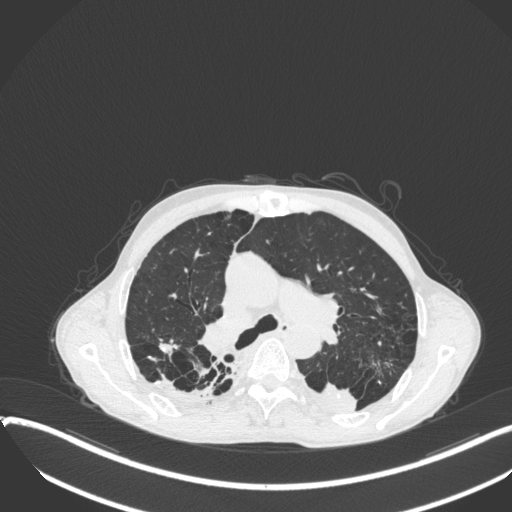
Chest CT, one axial slice. Position 254 of 400 along the scan axis. Reconstruction kernel B31f. 120 kVp. Lung window (W 1500 / L -600 HU). 1 mm slice thickness. 512 × 512 image matrix. Patient: male, 57 years. Case-level facts recorded for this patient, not image findings: clinical TNM (as recorded): T4 N0 M0.
Outlined on this slice (rectangle marked by the reading radiologist):
- lung tumour (recorded histology: squamous cell carcinoma): bounding box (x1, y1, x2, y2) in pixels: (296, 371, 359, 417)